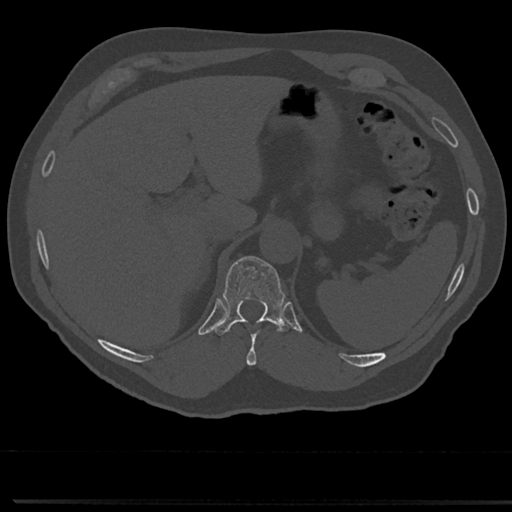
CT including the spine, one axial slice. 120 kVp. Bone window (W 1800 / L 400 HU). 0.5 mm slice thickness. 512 × 512 image matrix. Male patient, age 61 years. From the clinical record (not read from this slice): primary cancer: prostate.
Structures marked on this image (semi-automatic segmentation, software-assisted and operator-edited):
- T10 vertebra: bounding box [x1, y1, x2, y2] px = [245, 321, 274, 366]
- T11 vertebra: [218, 256, 285, 334]